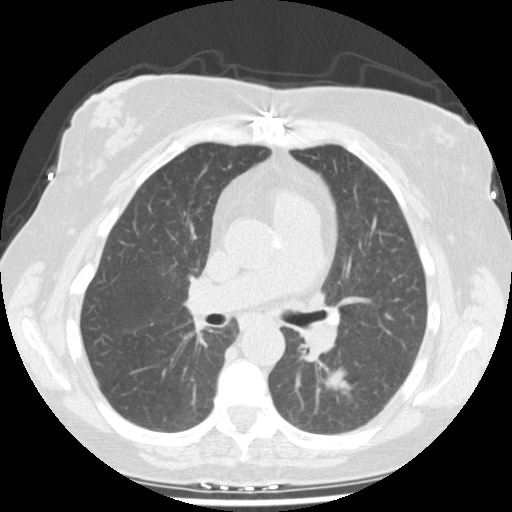
Low-dose screening chest CT, one axial slice. Position 98 of 159 along the scan axis. Lung window (W 1500 / L -600 HU). 512 × 512 image matrix, field of view 326 × 326 mm.
Structures marked on this image (expert manual segmentation):
- lesion 1 (tumor, lower lobe of left lung): bounding box (x1, y1, x2, y2) in pixels: (325, 370, 353, 395)